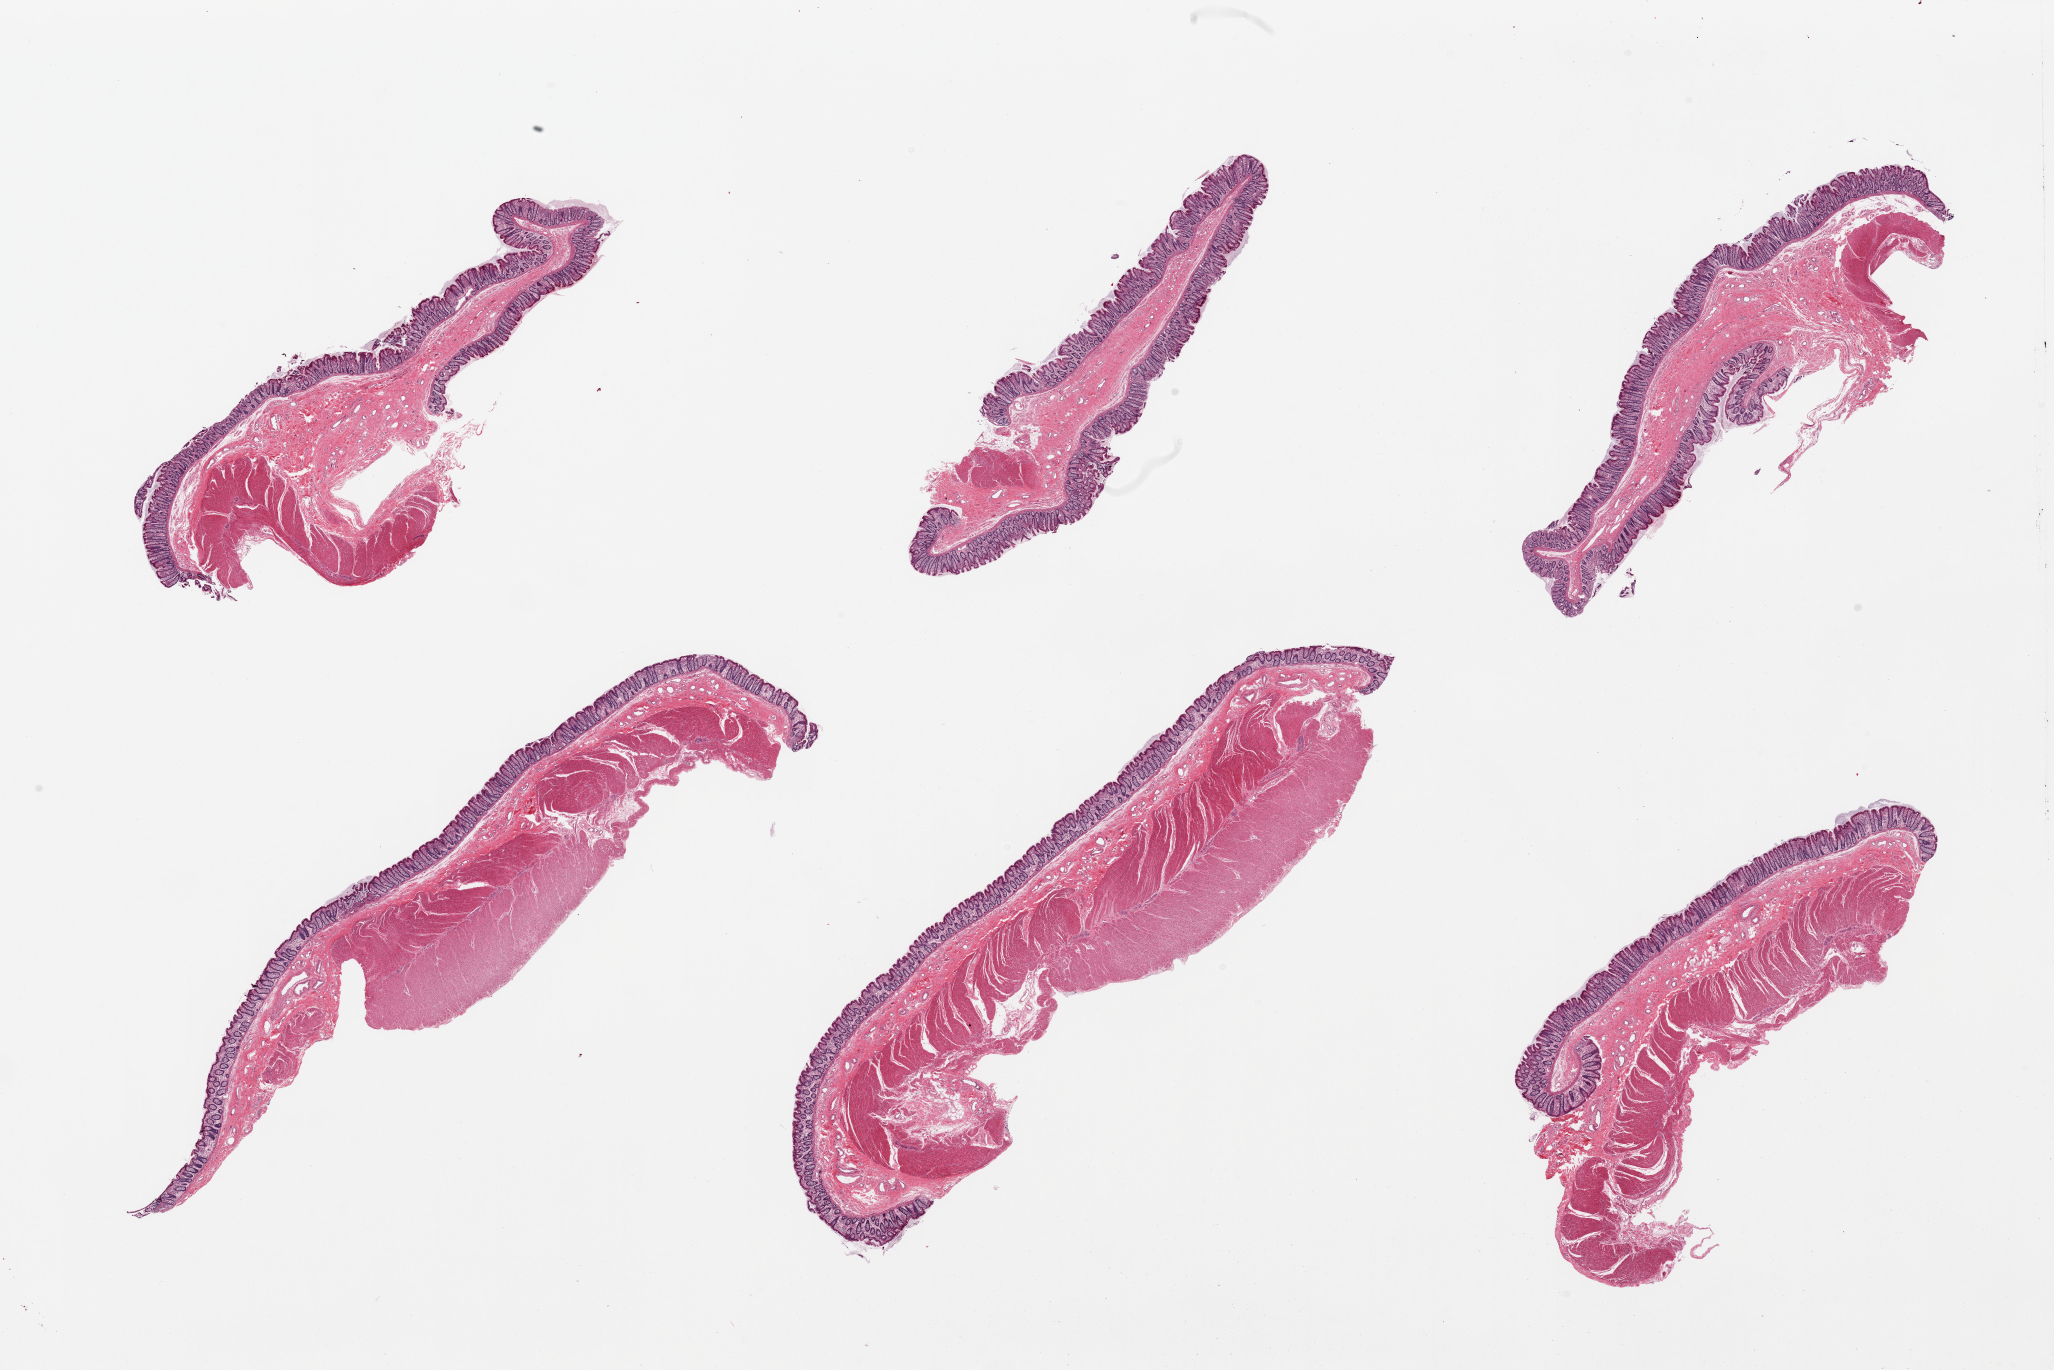
Whole-slide image, hematoxylin and eosin (H&E) stain, brightfield, low-resolution overview of the scanned area, about 32.5 x 21.7 mm. PAXgene-fixed, paraffin-embedded tissue. Target tissue: transverse colon. Donor tissue sample. Donor sex: female.
Reviewer comment on this tissue sample: 6 pieces, mucosa and muscularis.